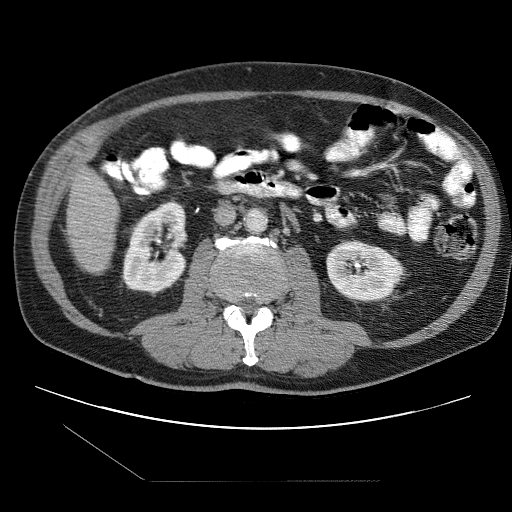
Contrast-enhanced abdominal CT (liver protocol), one axial slice. Position 18 of 109 along the scan axis. One of 2 acquisitions stored at this slice position. Soft-tissue window (W 400 / L 40 HU). 512 × 512 image matrix. Case-level facts recorded for this patient, not image findings: diagnosis: hepatocellular carcinoma (patient treated with transarterial chemoembolisation; whether this scan precedes or follows treatment is not stated here); TNM stage (as recorded): Stage-IIIB; Child-Pugh class: A; tumour differentiation: well differentiated; tumour nodularity: multinodular.
Annotated regions visible in this slice (semi-automatic segmentation, software-assisted and operator-edited):
- liver parenchyma outside the tumour (the mass and vessels are separate outlines, so this box may not span the whole liver): bounding box [x1, y1, x2, y2] px = [68, 166, 118, 270]